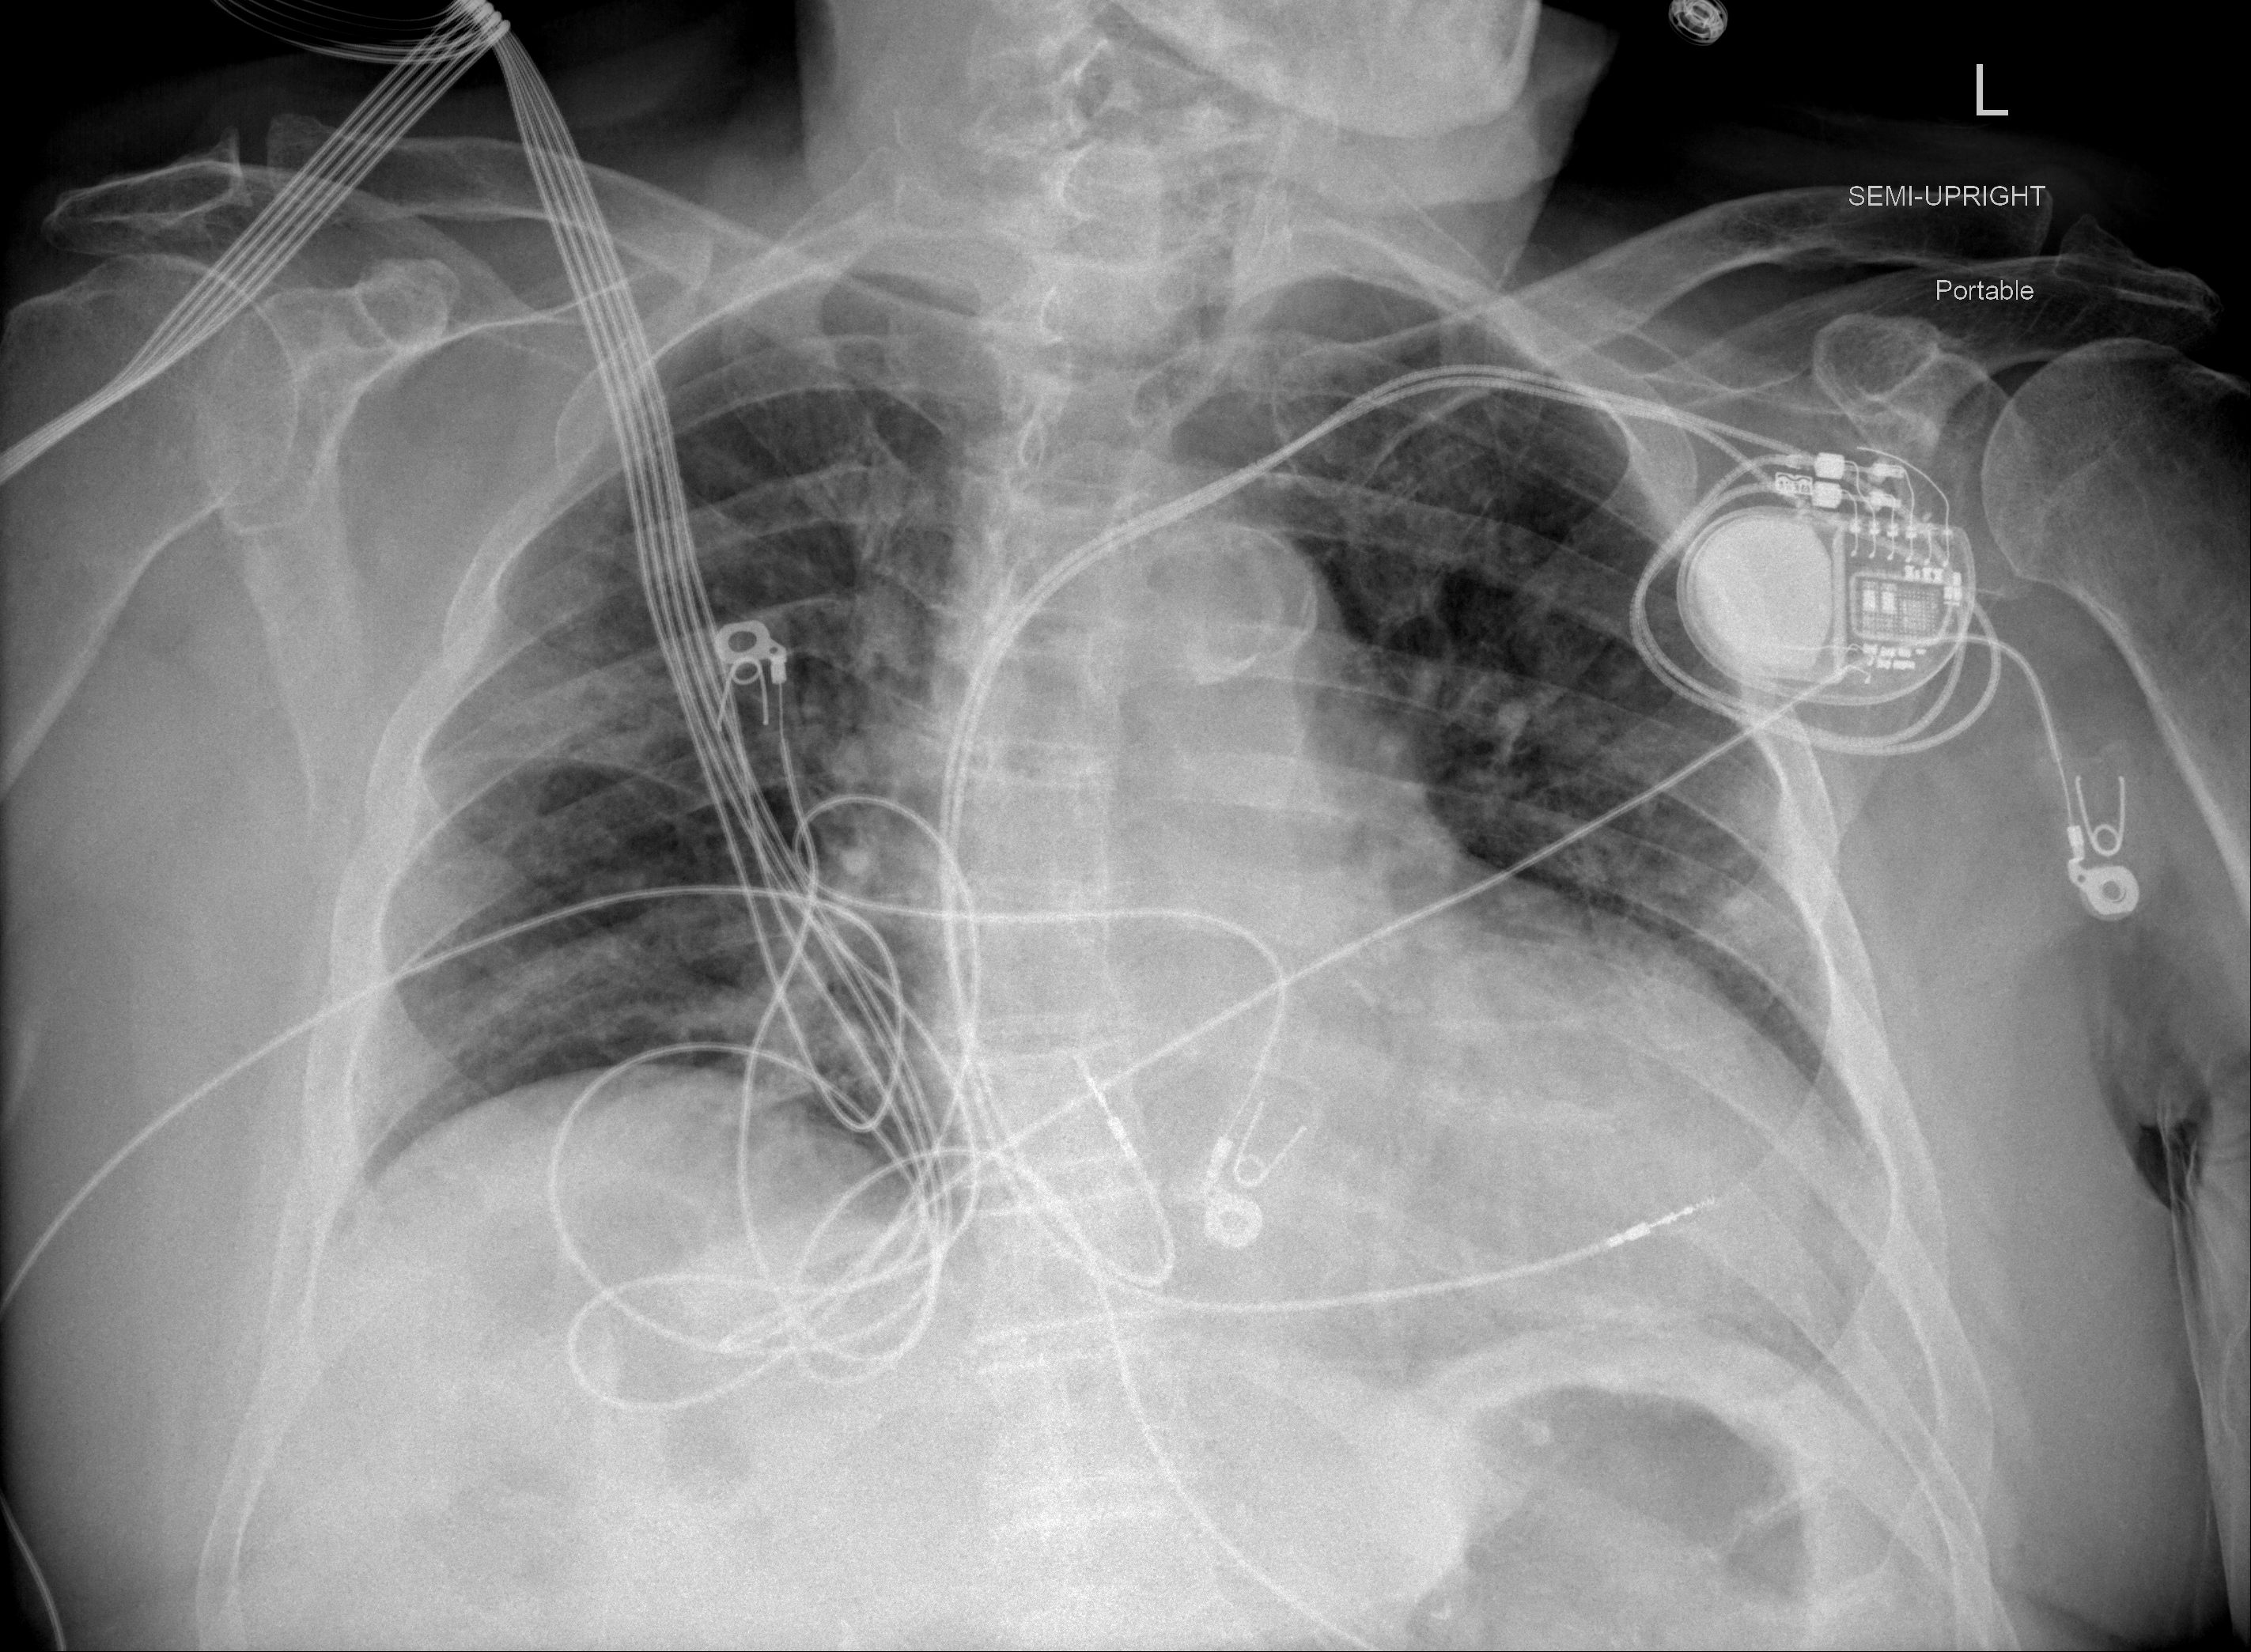
Chest X-ray (portable), AP projection. Male patient, age 88 years; imaged 5 days after the COVID-19 diagnosis.
Radiologist's key findings for this exam: Trace peribronchovascular airspace disease is noted within the right upper lobe, otherwise the lungs are clear without focal consolidation.